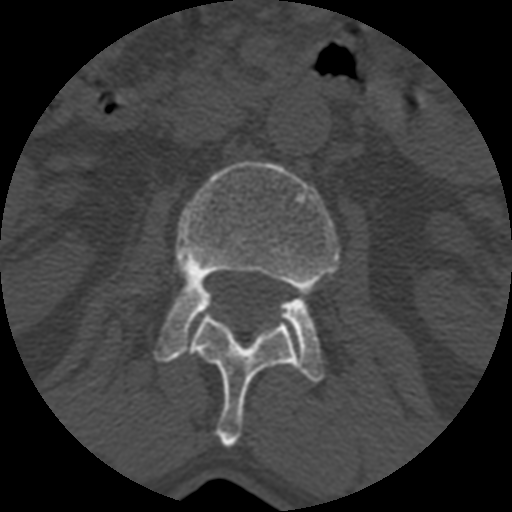
CT including the spine, one axial slice. Slice 345 of 399 in the series (ordered by position). 120 kVp. Bone window (W 1800 / L 400 HU). 1.25 mm slice thickness. 512 × 512 image matrix. Patient age 71 years. Case-level facts recorded for this patient, not image findings: primary cancer: prostate.
Outlined on this slice (semi-automatically segmented with operator editing):
- L1 vertebra: box from (x=186, y=313) to (x=297, y=446) px
- L2 vertebra: (x=155, y=160)–(x=339, y=382)